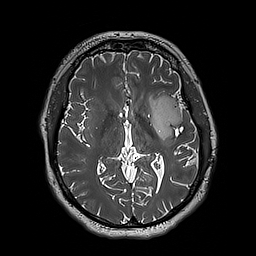
Brain MRI from a brain-tumour surgery series, one axial slice; position 104 of 192 along the scan axis; 1 mm slice thickness; 256 × 256 image matrix, field of view 250 × 250 mm. Case-level facts recorded for this patient, not image findings: histopathology: Astrocytoma; WHO grade: 3; IDH mutation: yes.
Outlined on this slice (expert manual segmentation):
- tumour: bounding box (x1, y1, x2, y2) in pixels: (147, 95, 183, 140)